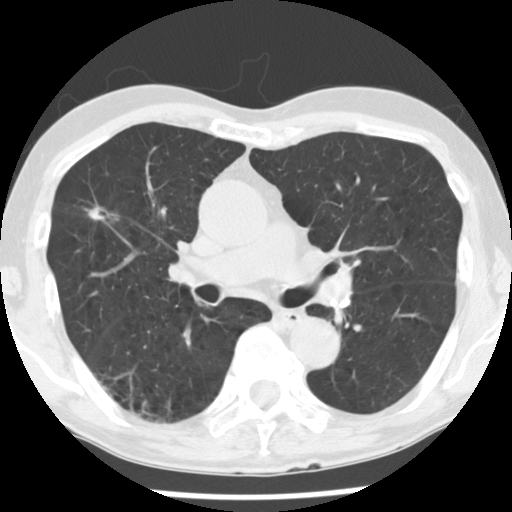
Low-dose screening chest CT, one axial slice. Slice 100 of 176 in the series (ordered by position). Reconstruction kernel STANDARD. 120 kVp. Lung window (W 1500 / L -600 HU). 2.5 mm slice thickness. 512 × 512 image matrix, field of view 309 × 309 mm.
Outlined on this slice (outlined manually by an expert reader):
- lesion 1 (tumor, upper lobe of right lung): bounding box (x1, y1, x2, y2) in pixels: (85, 204, 108, 222)